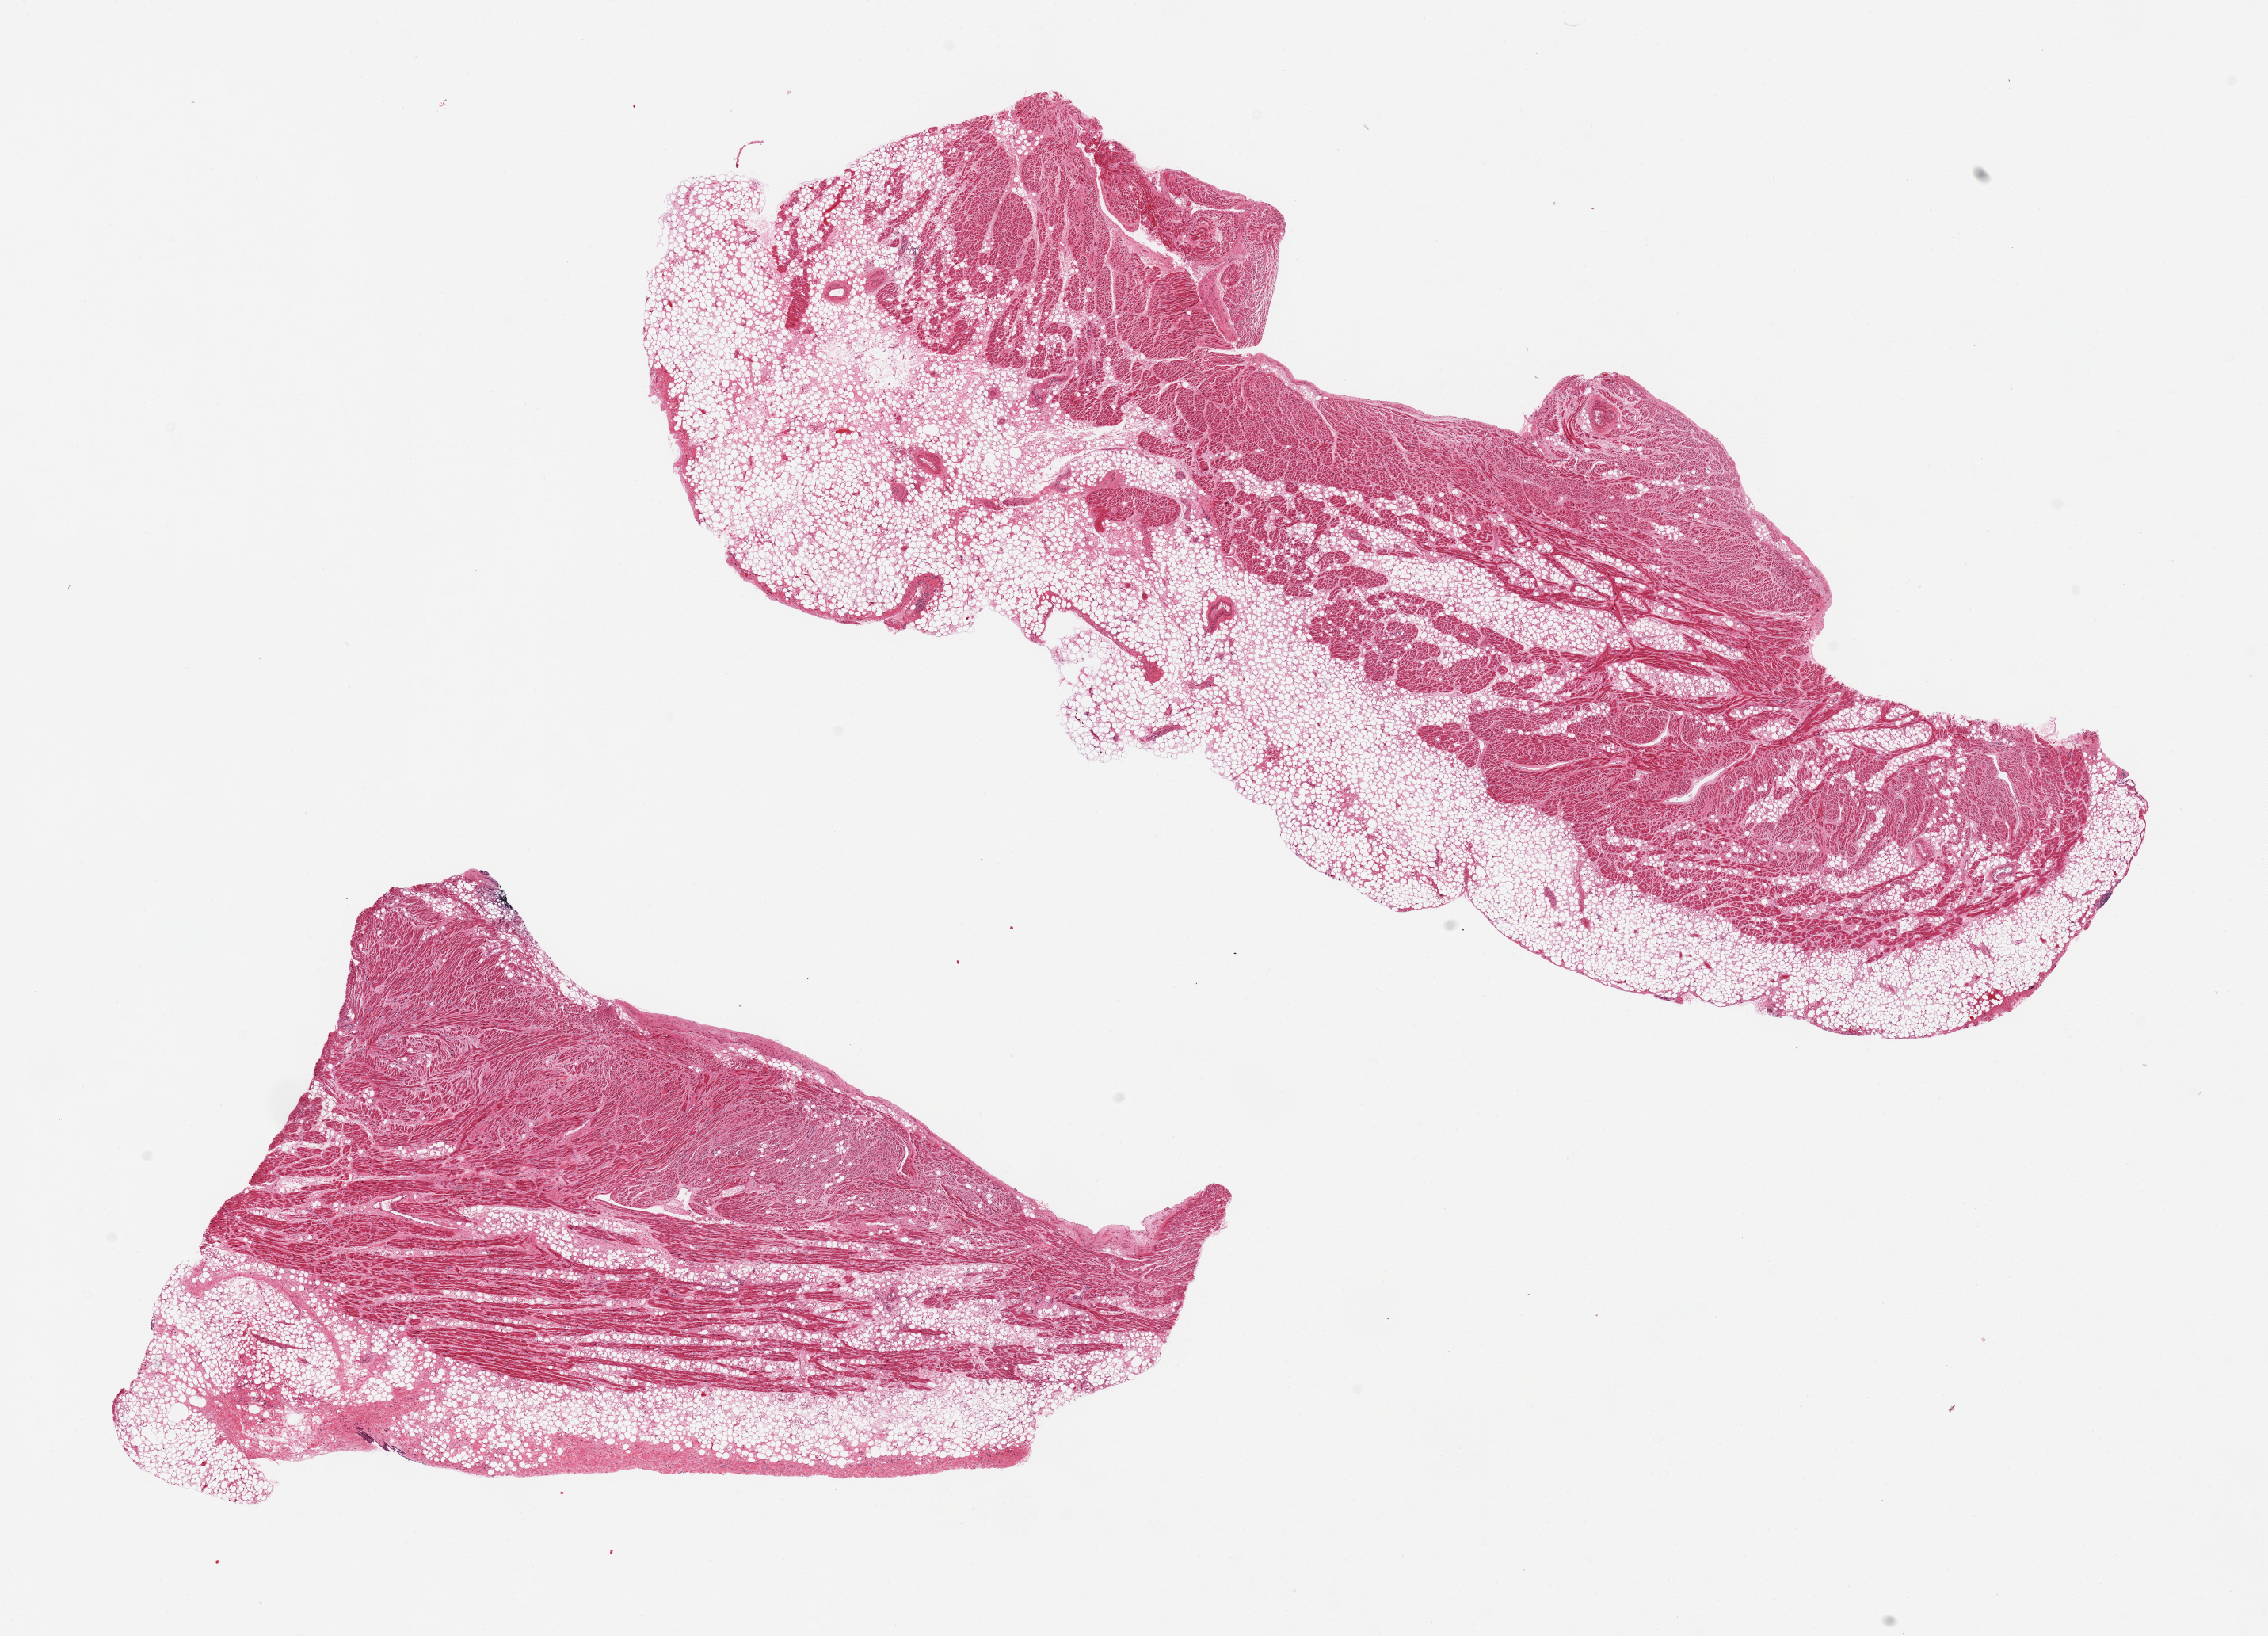
Hematoxylin and eosin (H&E) whole-slide image, shown as a low-resolution overview of the whole scanned area (about 22.6 x 16.3 mm, slide scanned at 20x), PAXgene-fixed paraffin-embedded (PFPE) section, target tissue: auricular appendage, tissue donor sample. Donor: female.
Review note (as recorded): 2 pieces; 50 and 30% external and internal fat.